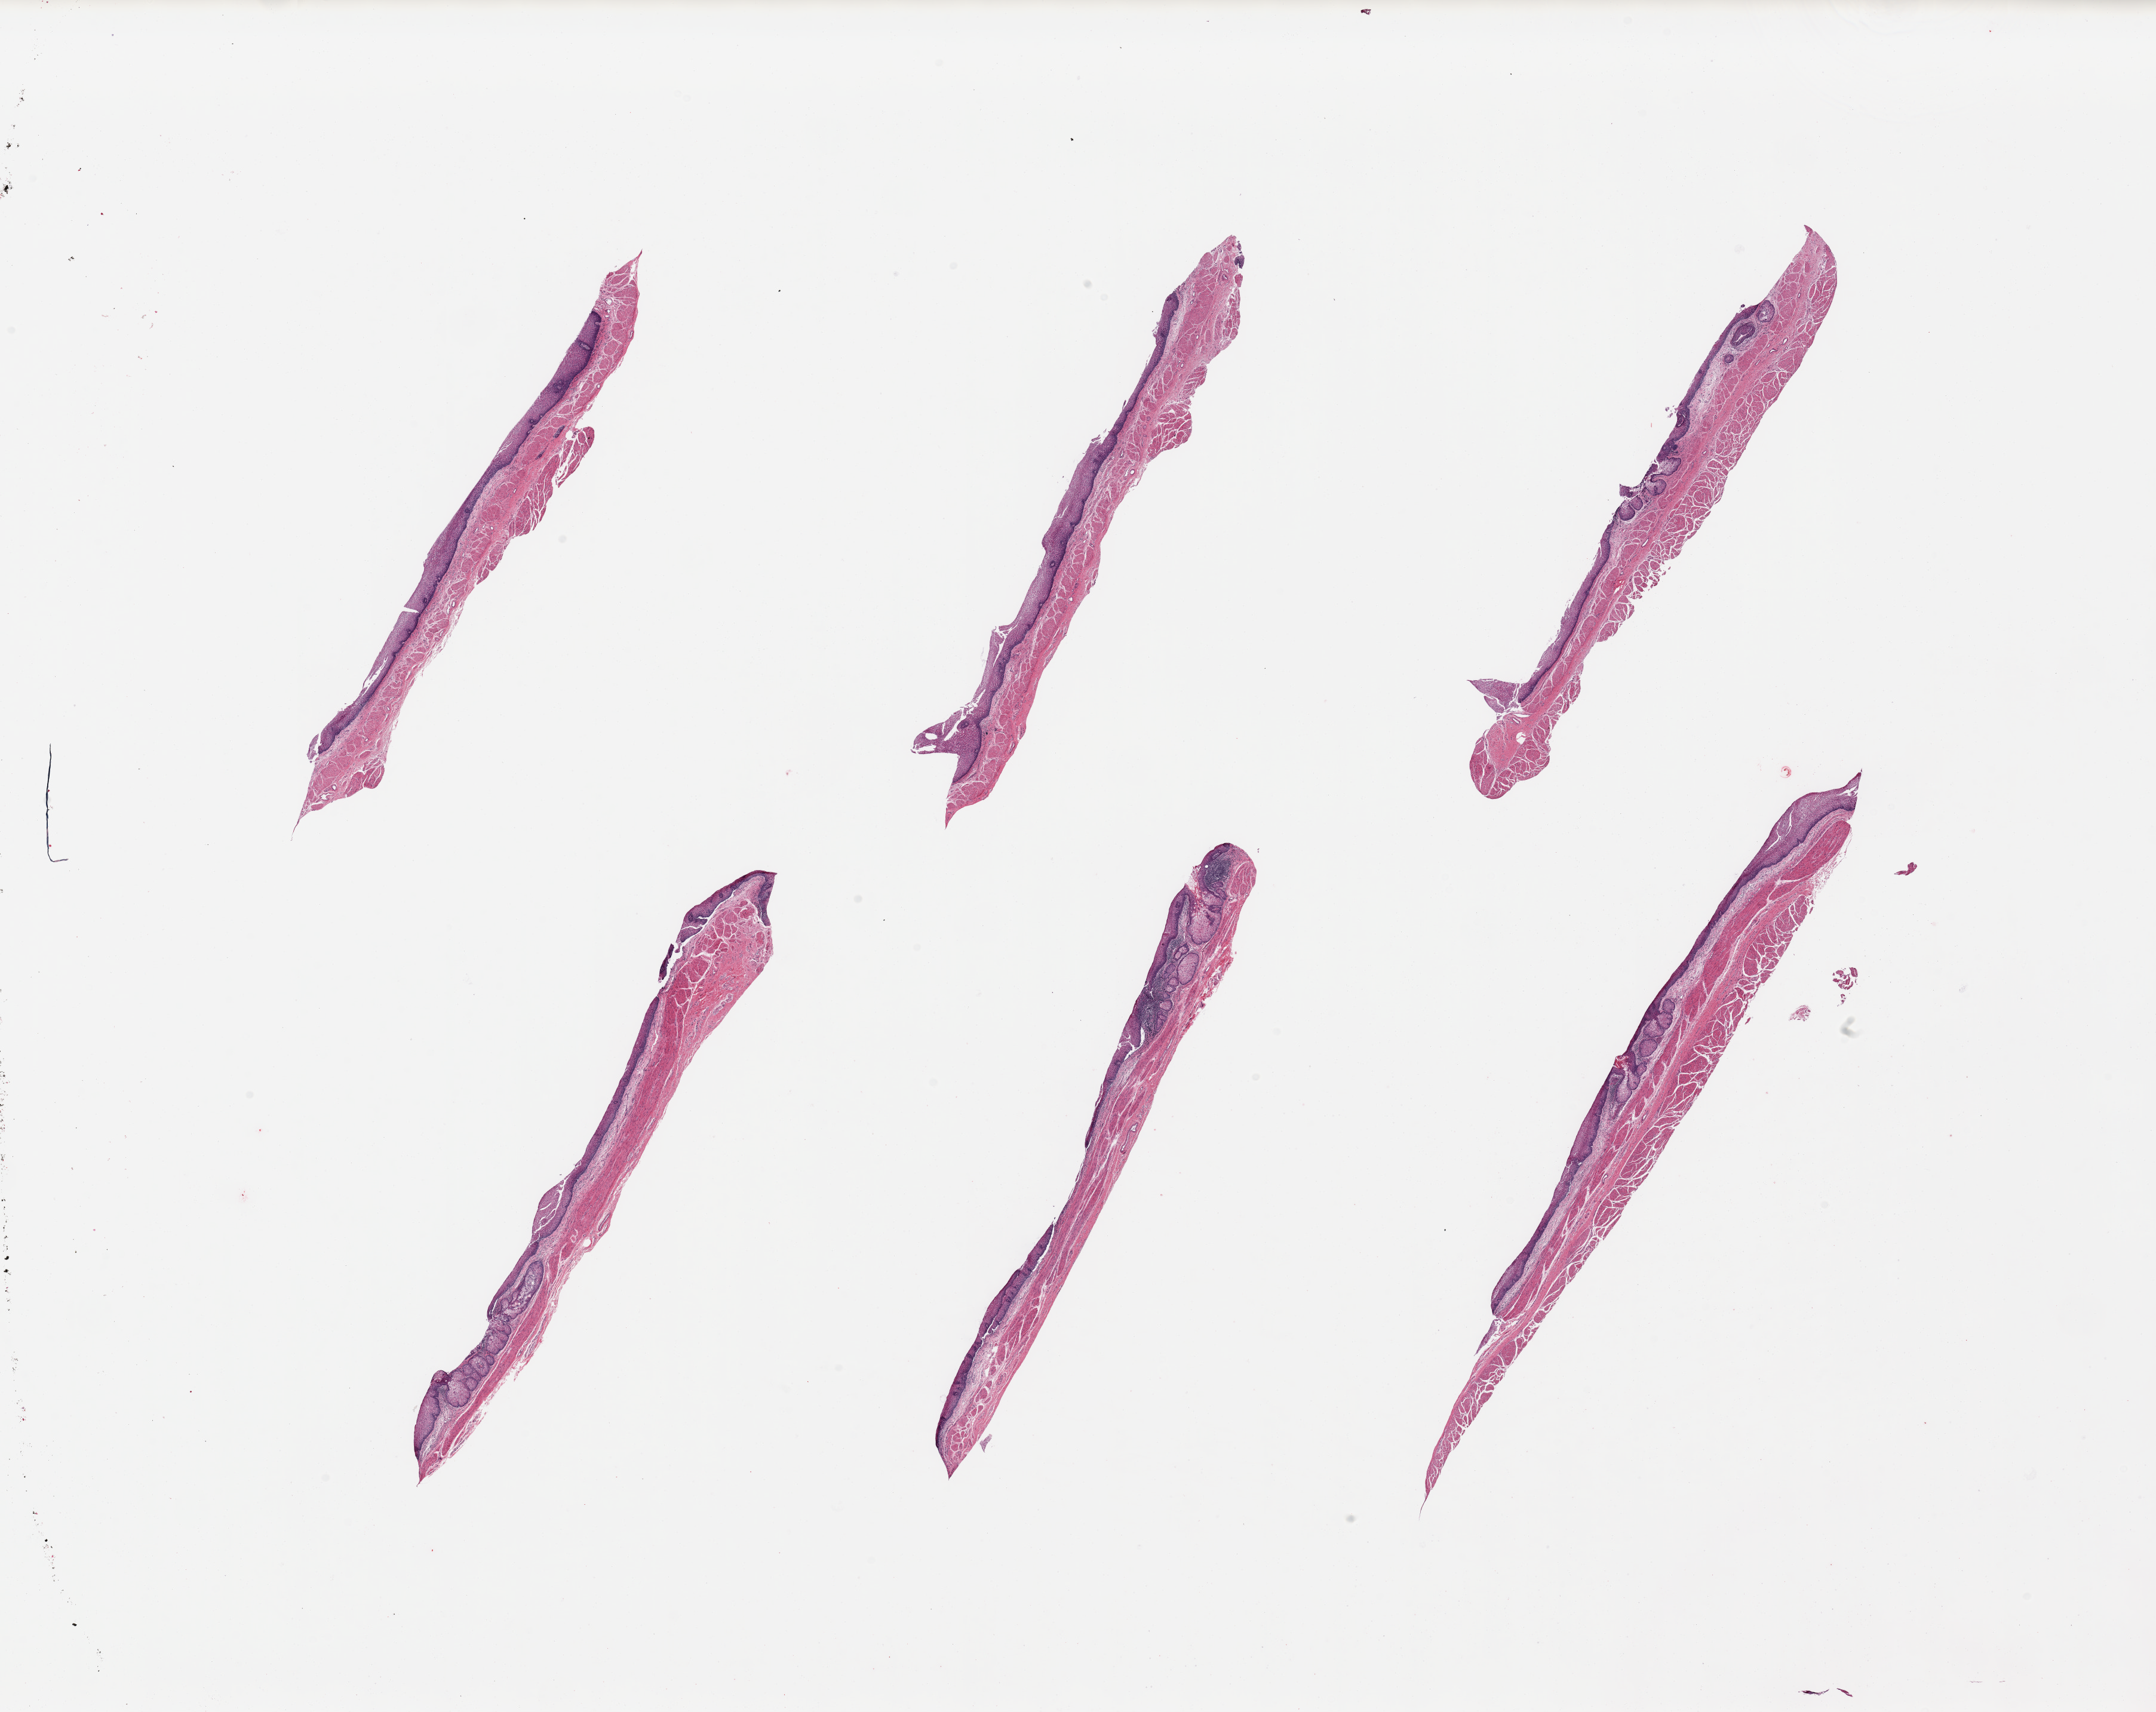
Digitized H&E-stained section — shown as a low-resolution overview of the whole scanned area (about 28.5 x 22.7 mm), PAXgene-fixed, paraffin-embedded tissue, section of esophageal mucous membrane (target tissue), tissue donor sample. Female donor.
Reviewer comment on this tissue sample: 6 pieces; large numbers of metaplastic/ectopic sebaceous glands, several pieces include muscularis propria.